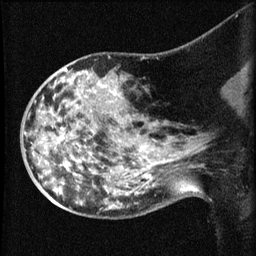
Breast MRI (dynamic contrast-enhanced), one sagittal slice; position 34 of 60 along the scan axis; dynamic contrast-enhanced series, image 2 of 3 at this slice position (ordered by acquisition); 1.5 T; TE 4.2 ms, TR 8.2 ms; 2.1 mm slice thickness; 256 × 256 image matrix. Female patient, age 50 years.
Structures marked on this image (semi-automatically segmented with operator editing):
- analysis volume of interest (the breast-tissue region the enhancement analysis was run in; not a lesion): bounding box <38,74,169,211> (left, top, right, bottom; pixels)
- tumour enhancement mask (voxels above the 70 % enhancement threshold inside the analysis volume of interest): <137,147,146,193>